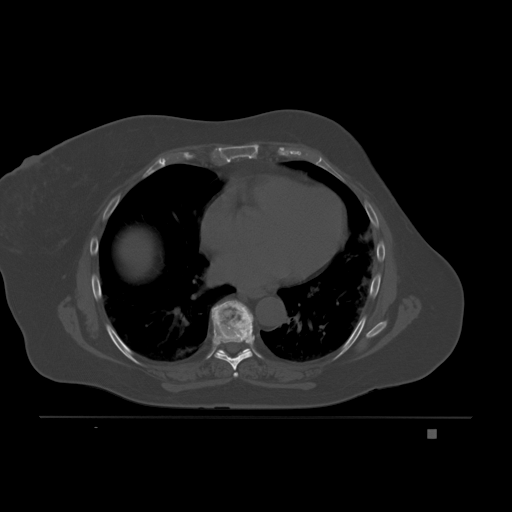
CT including the spine, one axial slice; position 125 of 221 along the scan axis; bone window (W 1800 / L 400 HU); 3 mm slice thickness; 512 × 512 image matrix, field of view 474 × 474 mm. Female patient, age 63 years. Case-level facts recorded for this patient, not image findings: primary cancer: breast.
Structures marked on this image (semi-automatically segmented with operator editing):
- T6 vertebra: bounding box (x1, y1, x2, y2) in pixels: (234, 373, 238, 377)
- T7 vertebra: (212, 300, 255, 377)
- T8 vertebra: (218, 348, 250, 355)